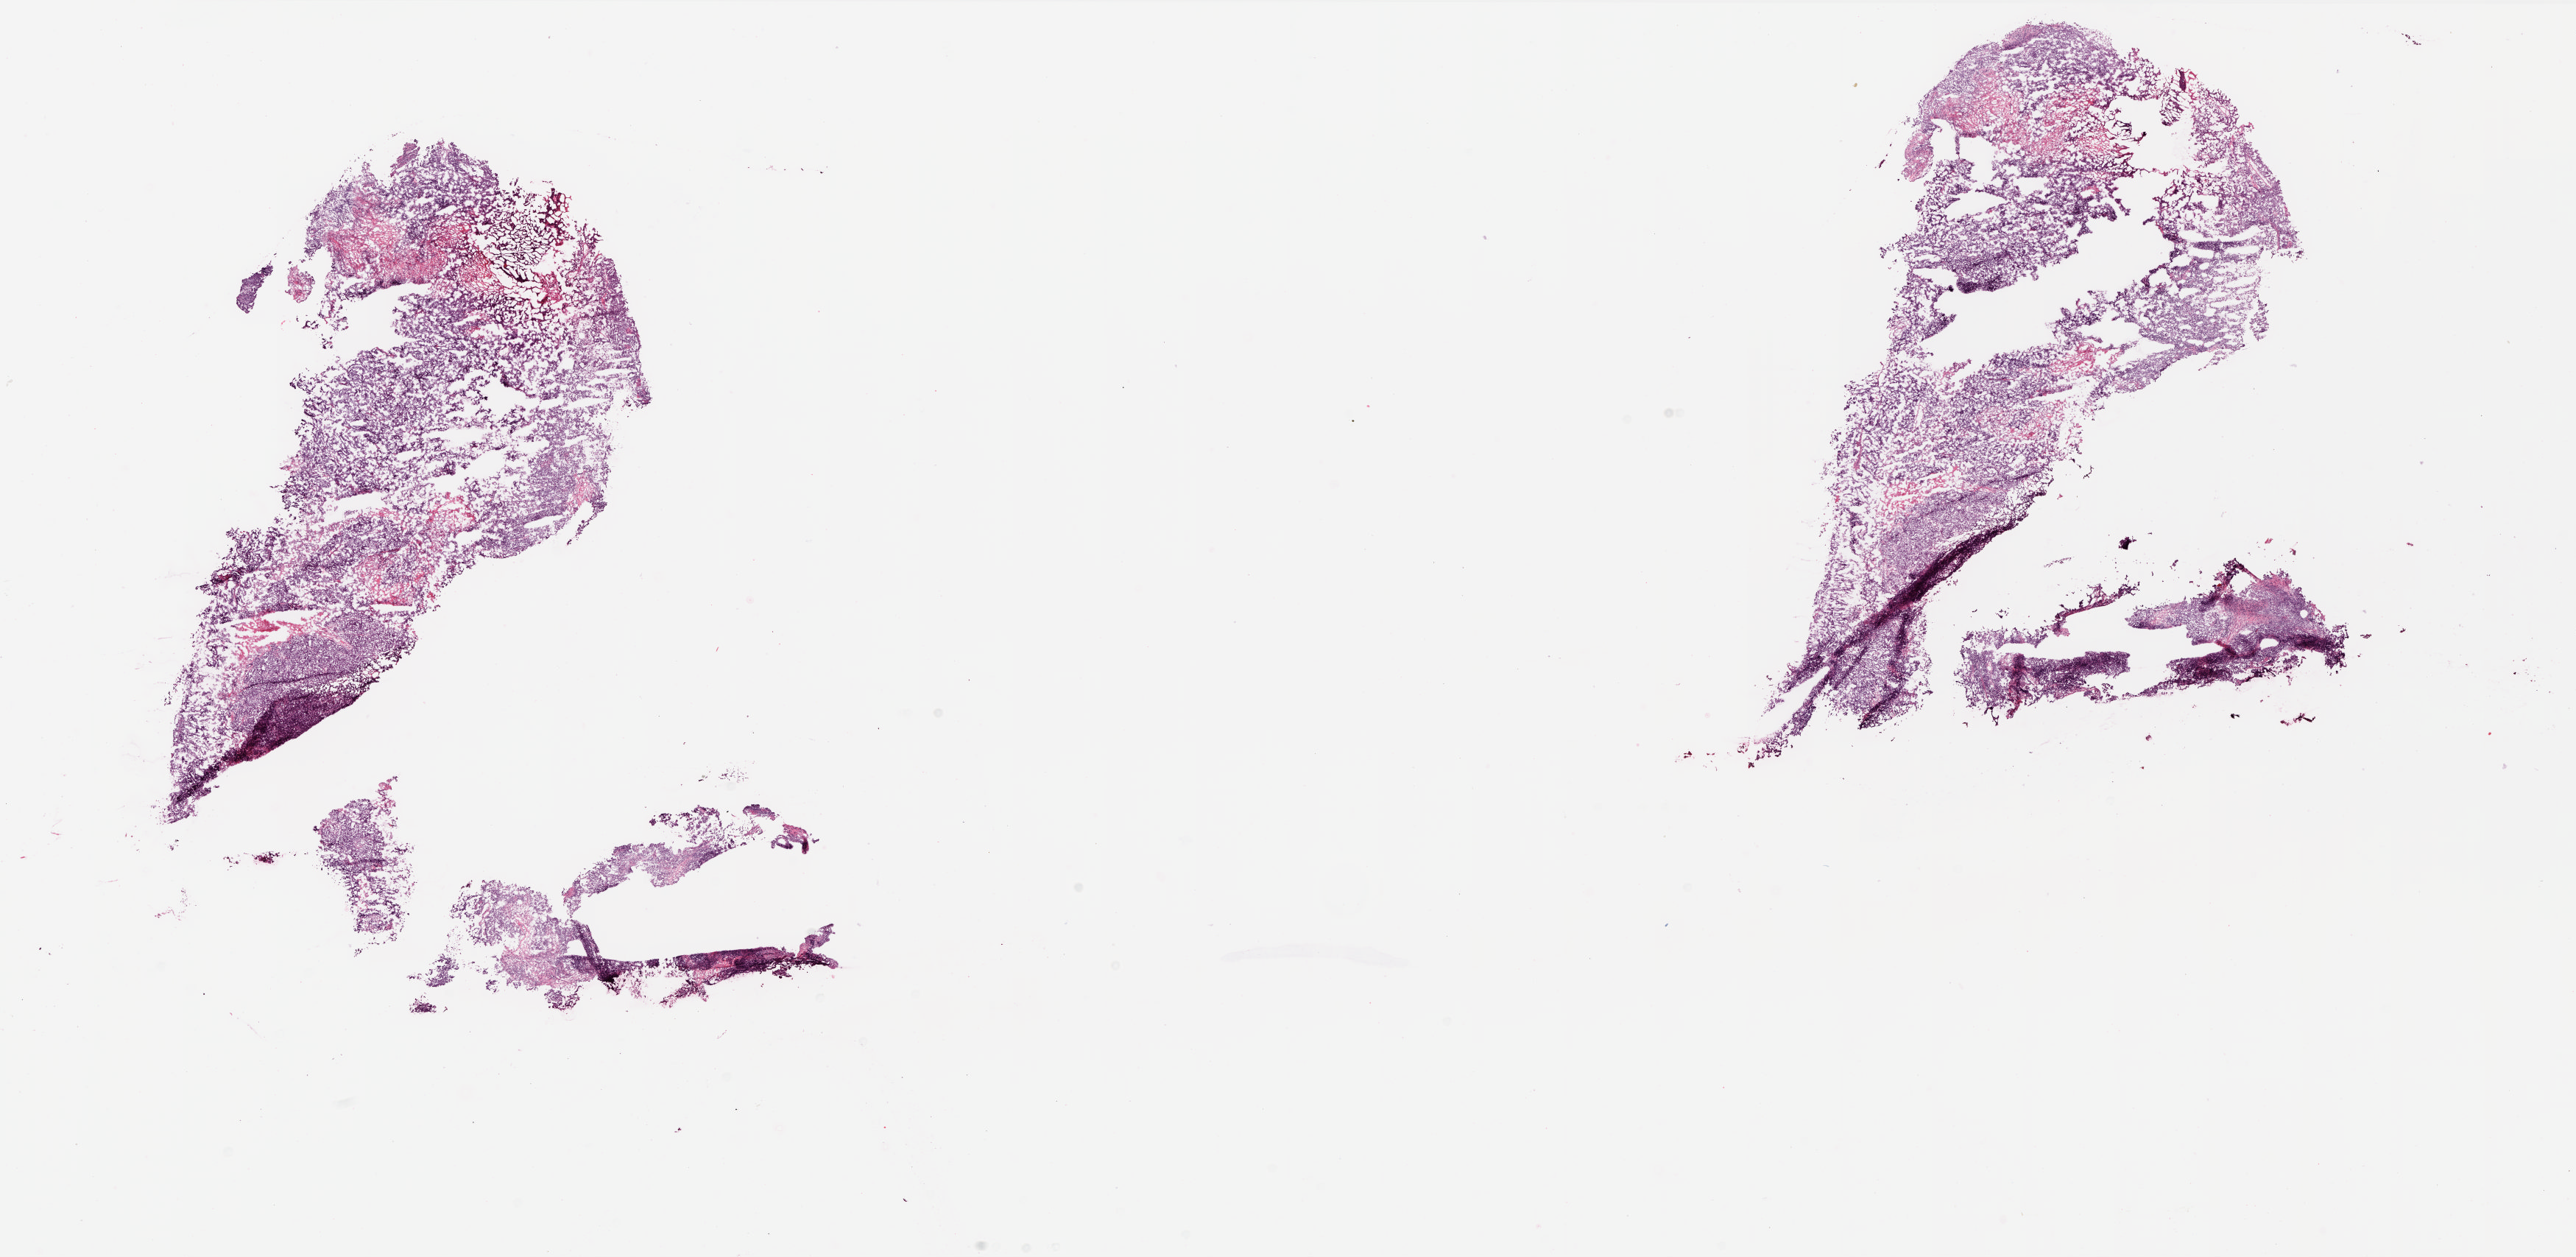
H&E whole-slide image, low-resolution overview of the scanned area, about 27.9 x 13.6 mm. Frozen section. Ovary, primary tumour sample. Female patient. Histologic grade: G3 (poorly differentiated). Pathologist review of this section (percent, as recorded): tumour cells 94%, tumour nuclei 95%, normal cells 0%, stromal cells 5%, necrosis 1%.
Diagnosis: Serous cystadenocarcinoma, NOS. FIGO stage: IIIB.